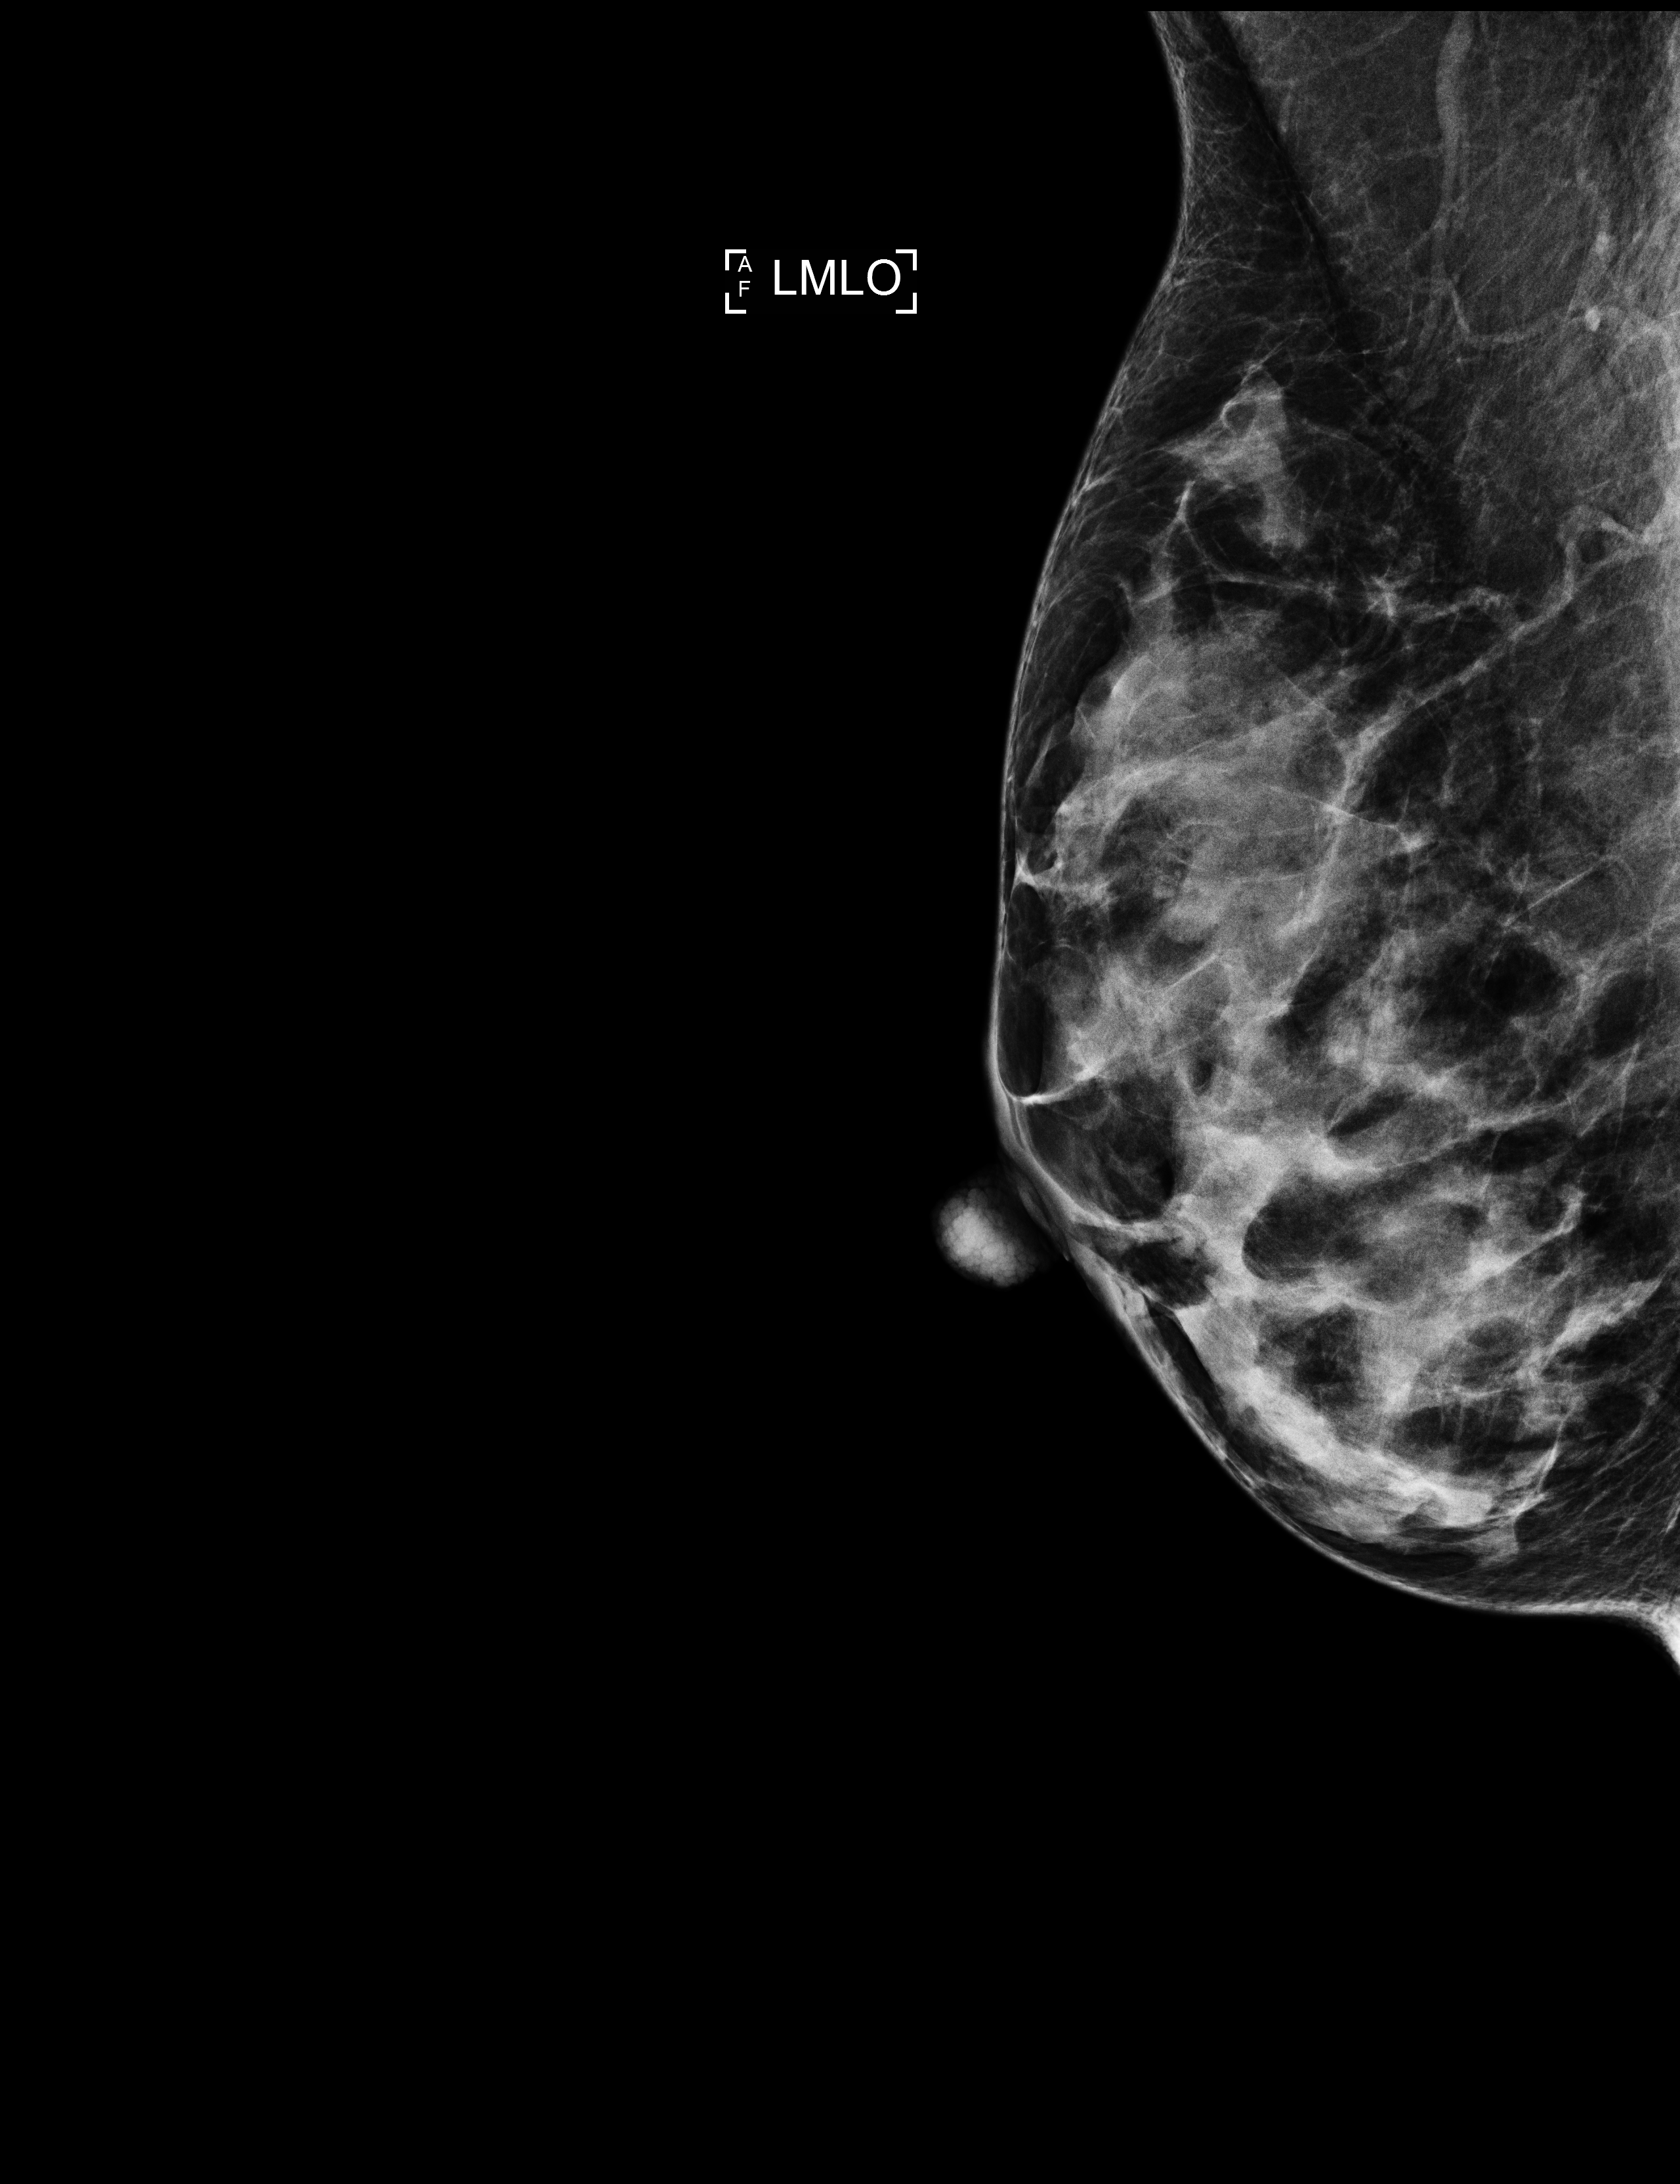
Digital mammogram (FFDM), left breast, MLO view, screening examination. Patient aged 53 years (female).
BI-RADS breast density category at the screening exam (both breasts, scale 1–4): 3. Final BI-RADS category for the screening round (tomosynthesis exam, both breasts): category 1. Recall: no recall after this screen.